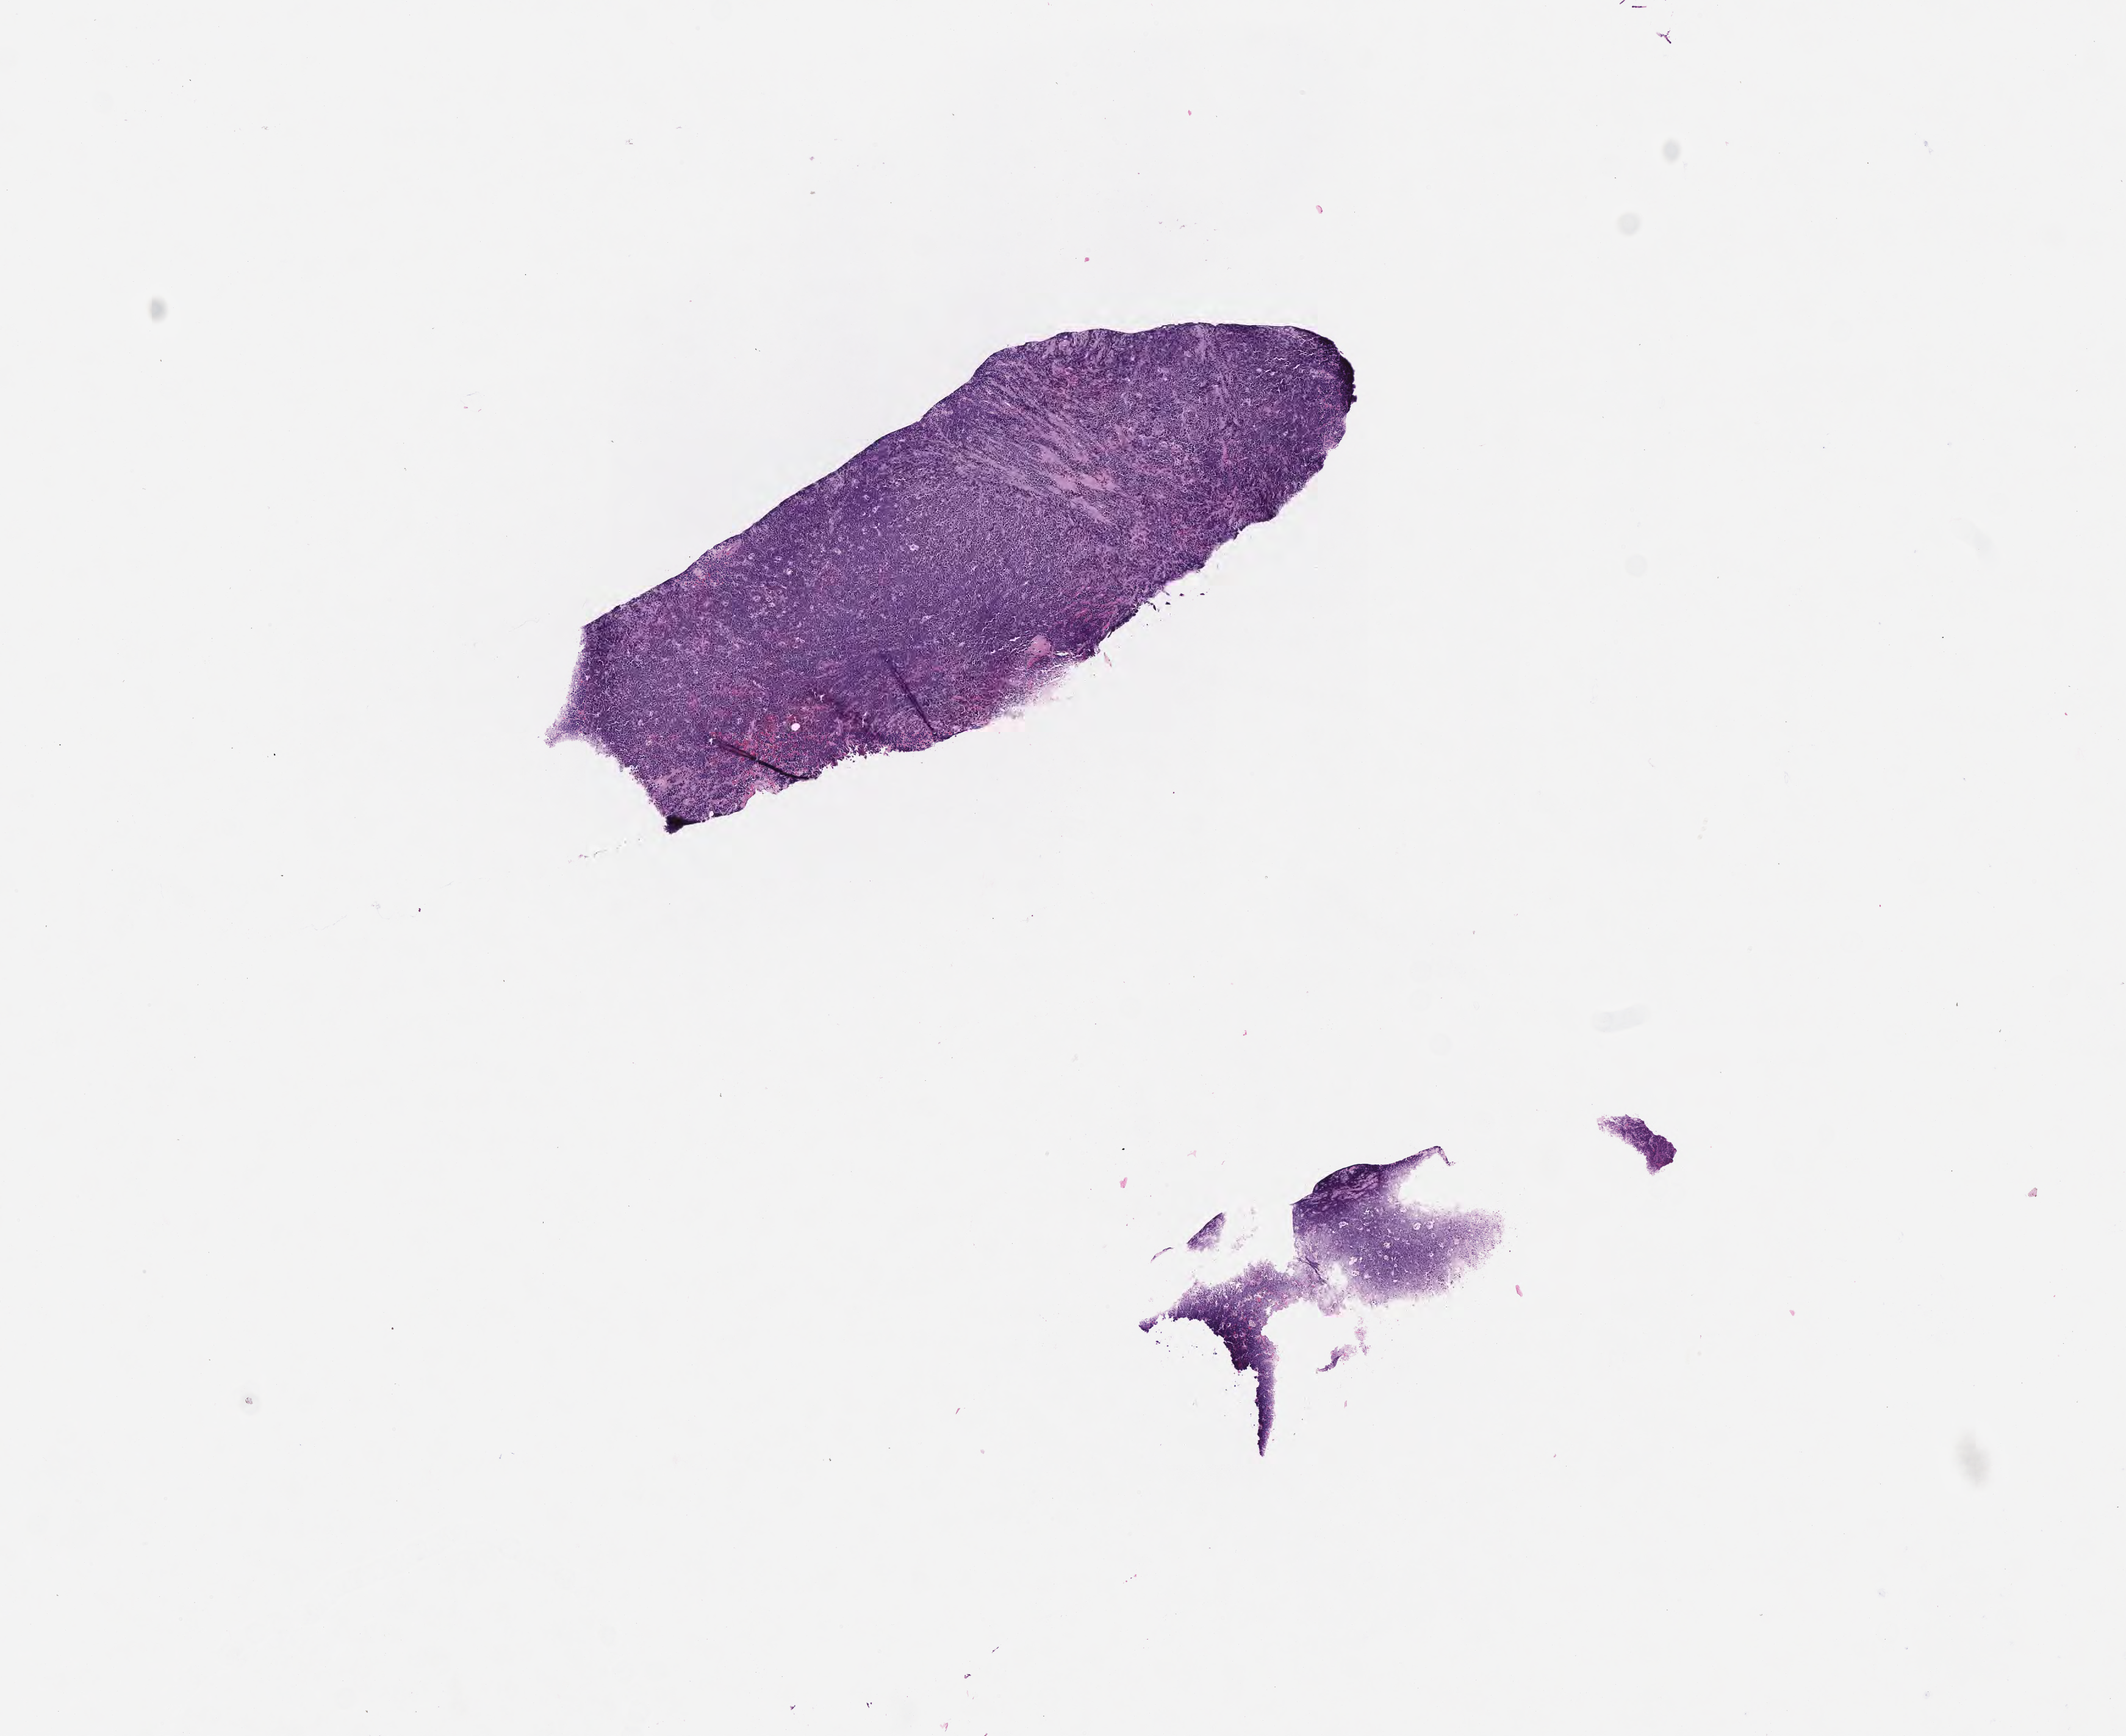
Whole-slide image, haematoxylin and eosin stain — a low-resolution overview of the entire scanned area, about 7.0 x 5.8 mm. Formalin-fixed, paraffin-embedded (FFPE) tissue. Primary tumor. Patient female; 46 years old. Pathologist review of this section (percent, as recorded): tumor cells 90%, tumor nuclei 95%.
Histologic diagnosis: Burkitt lymphoma, NOS.